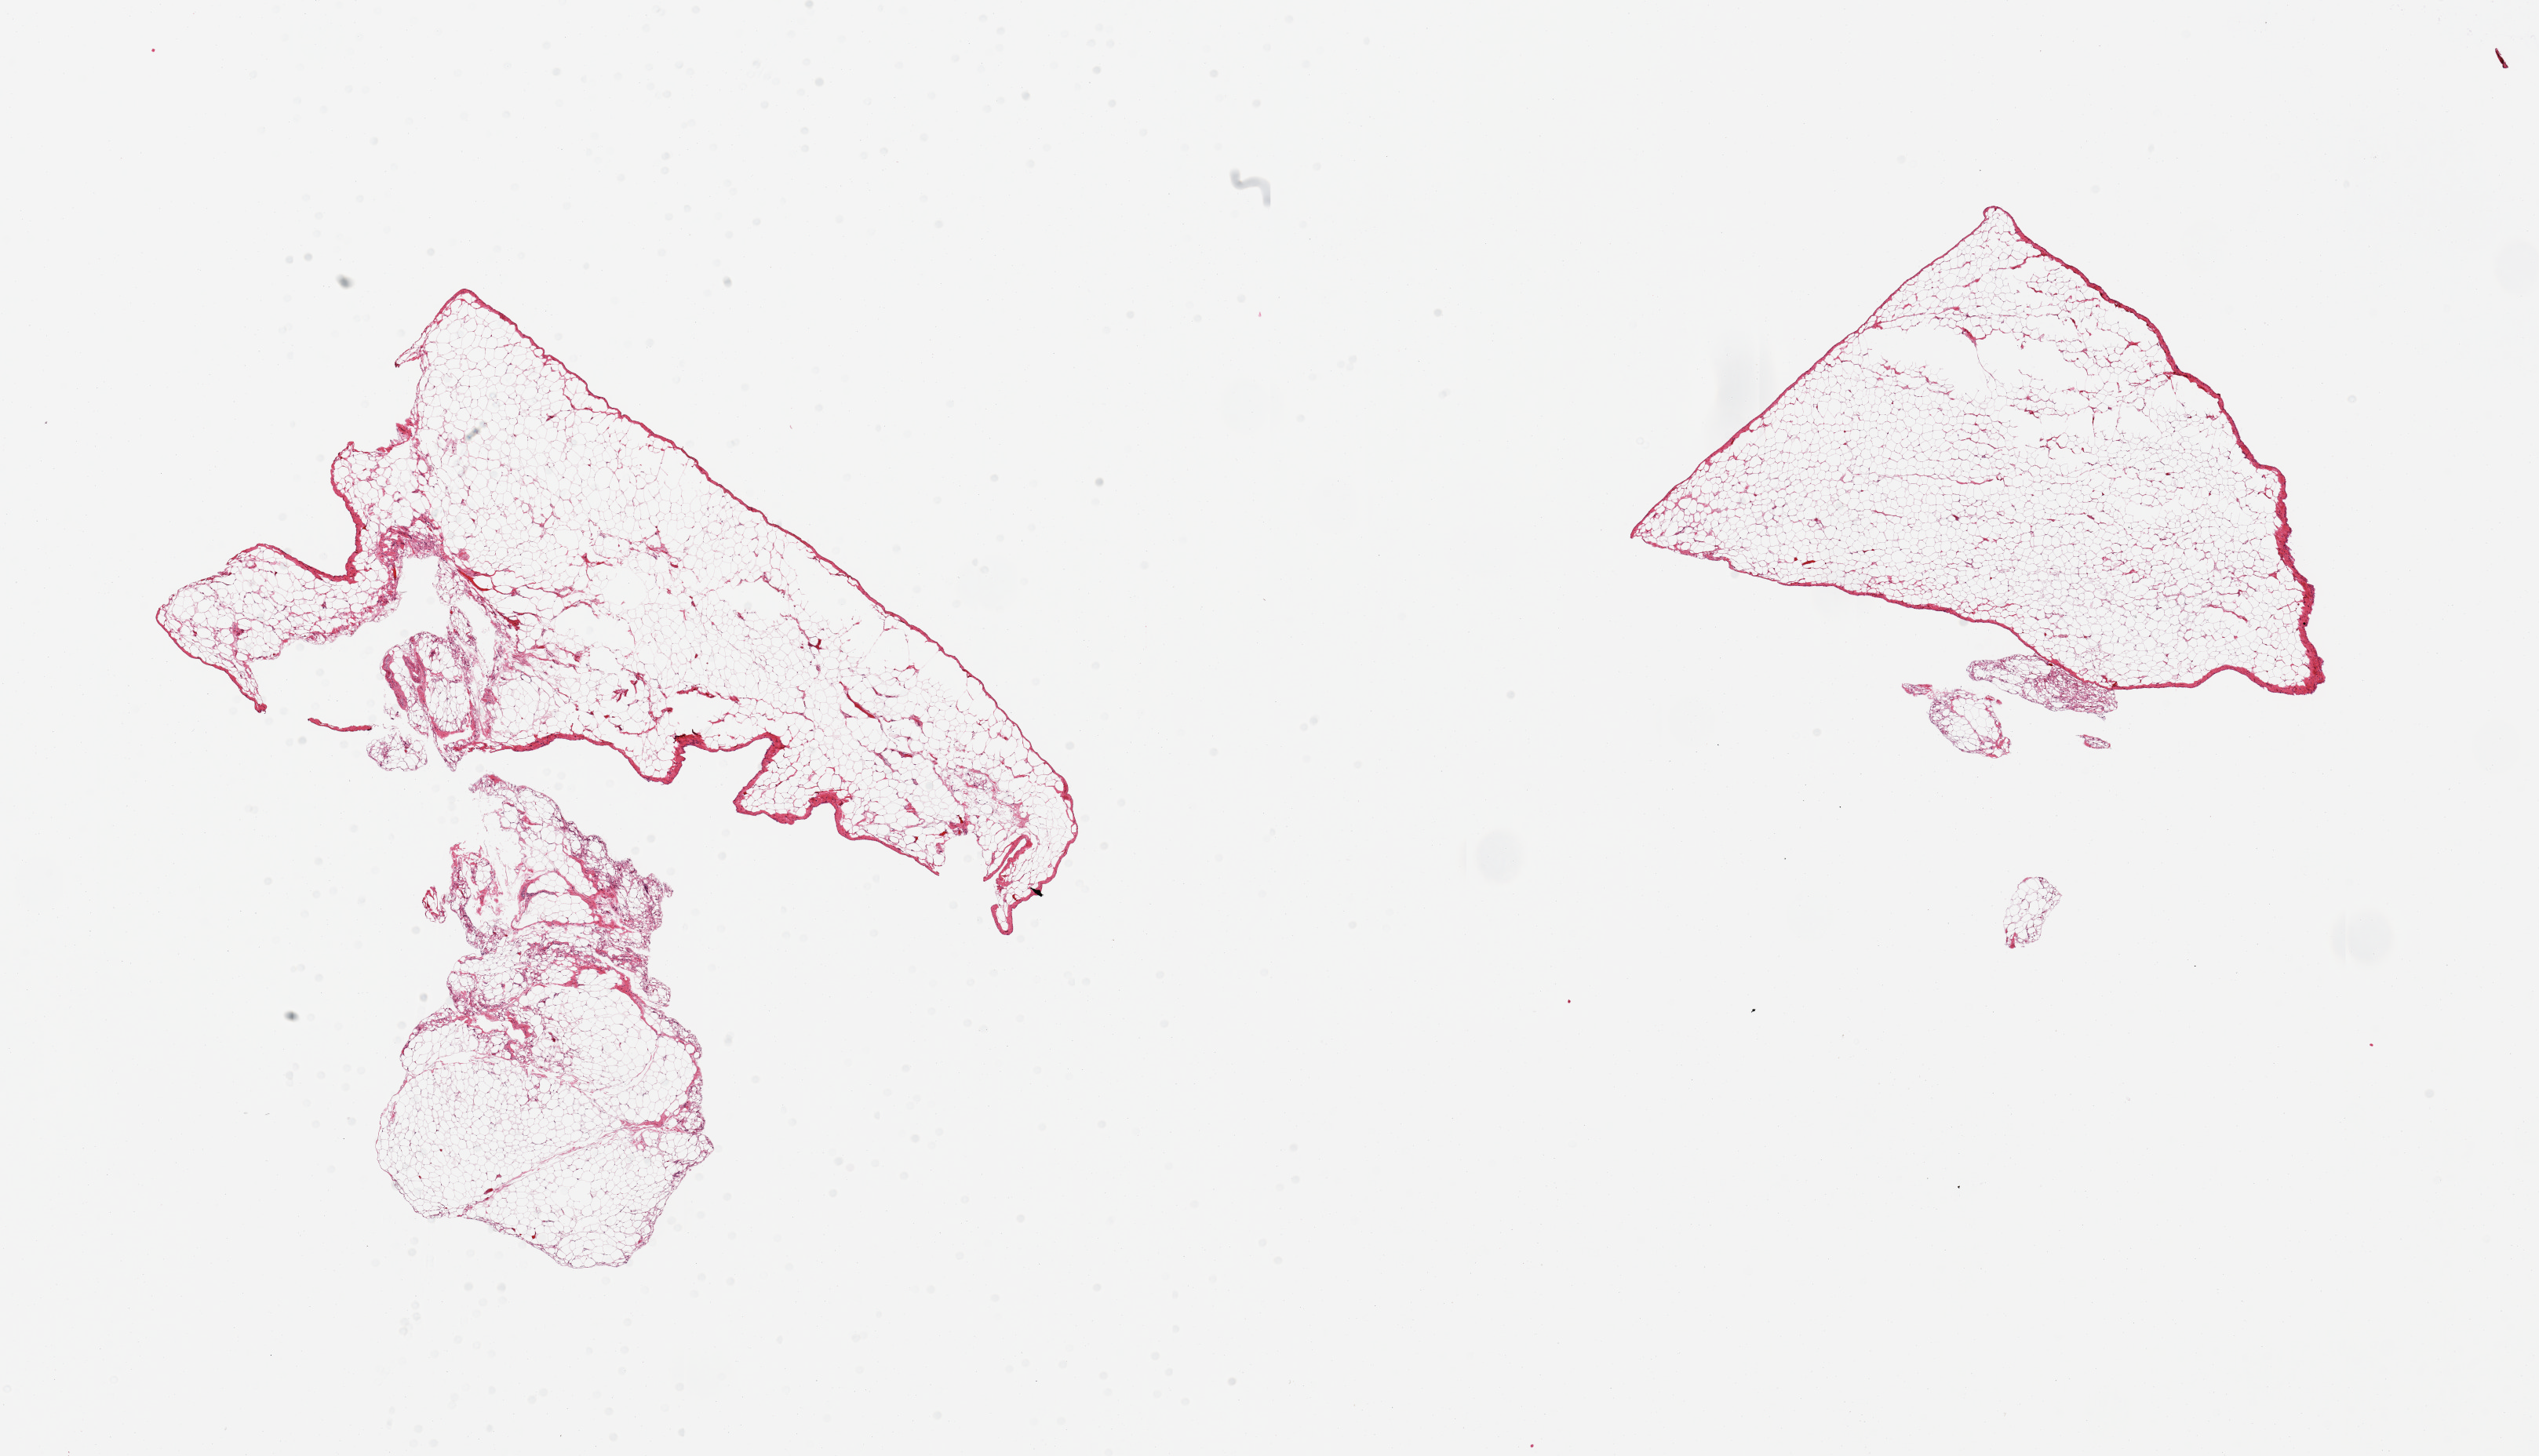
Digitized H&E-stained section — shown as a low-resolution overview of the whole scanned area (about 25.6 x 14.7 mm), PAXgene-fixed, paraffin-embedded tissue, section of omentum (target tissue), tissue donor sample. Donor: male.
Review note (as recorded): 2 pieces.